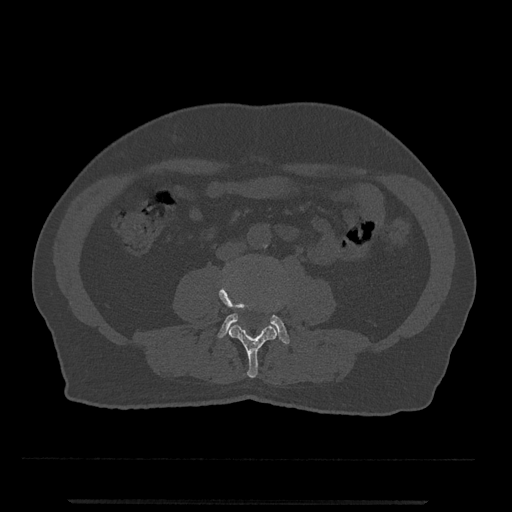
CT including the spine, one axial slice. Slice 175 of 797 in the series (ordered by position). Reconstruction kernel Br40s/3. 120 kVp. Bone window (W 1800 / L 400 HU). 512 × 512 image matrix, field of view 419 × 419 mm. Patient: male, 63 years. From the clinical record (not read from this slice): primary cancer: prostate.
Annotated regions visible in this slice (semi-automatic segmentation, software-assisted and operator-edited):
- L3 vertebra: bounding box (x1, y1, x2, y2) in pixels: (219, 271, 277, 378)
- L4 vertebra: (218, 314, 290, 344)